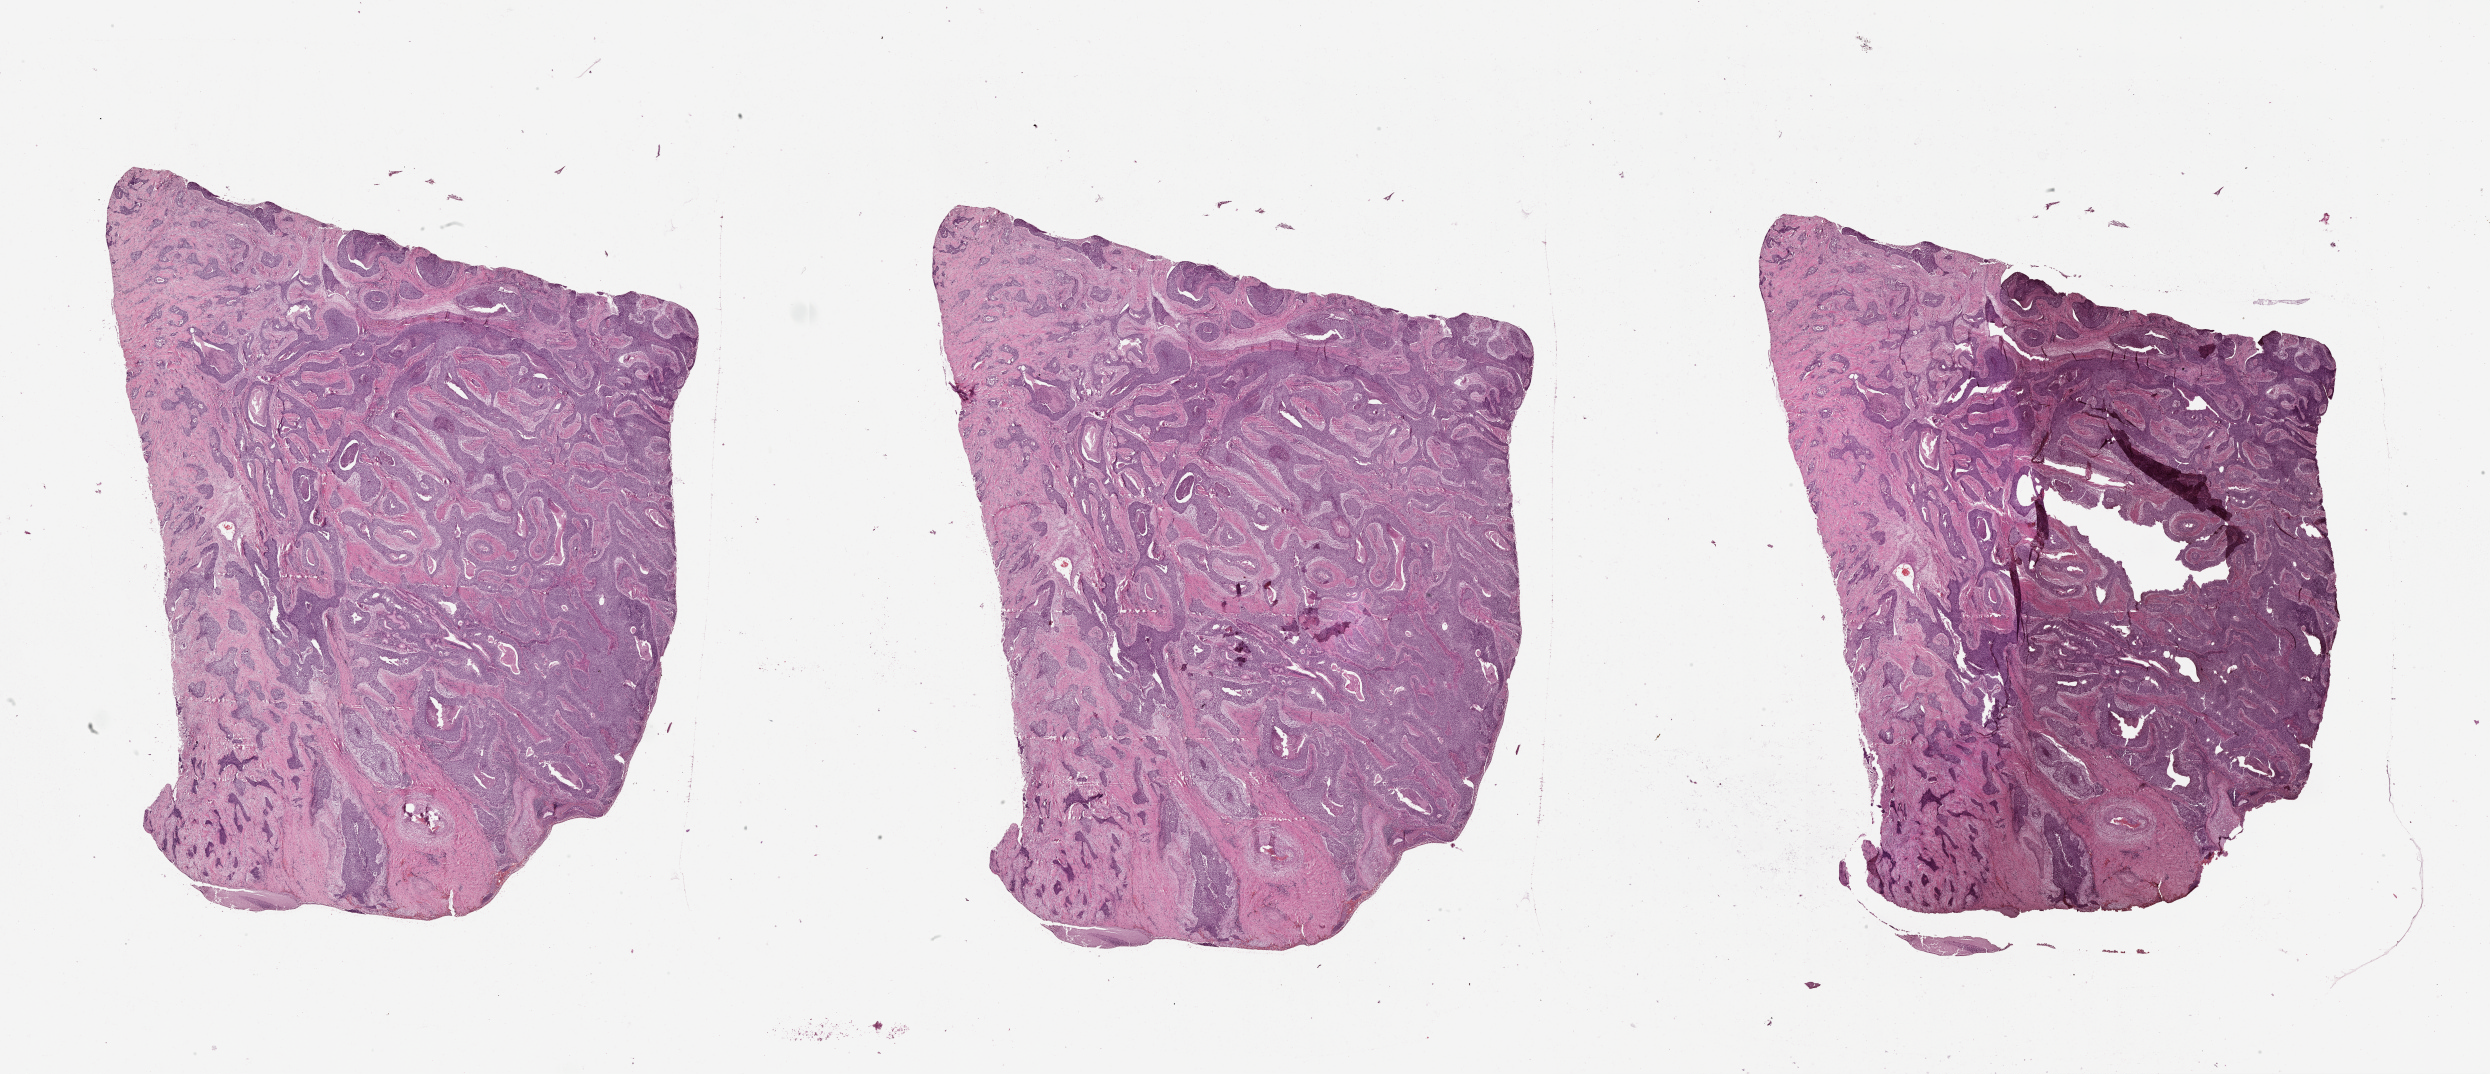
H&E-stained whole-slide image — whole scanned area (about 40.1 x 17.3 mm, slide scanned at 20x) shown as a low-resolution overview, tumour tissue sample, lung. 63-year-old male patient.
• patient diagnosis (cohort enrolment): squamous cell carcinoma (lung)